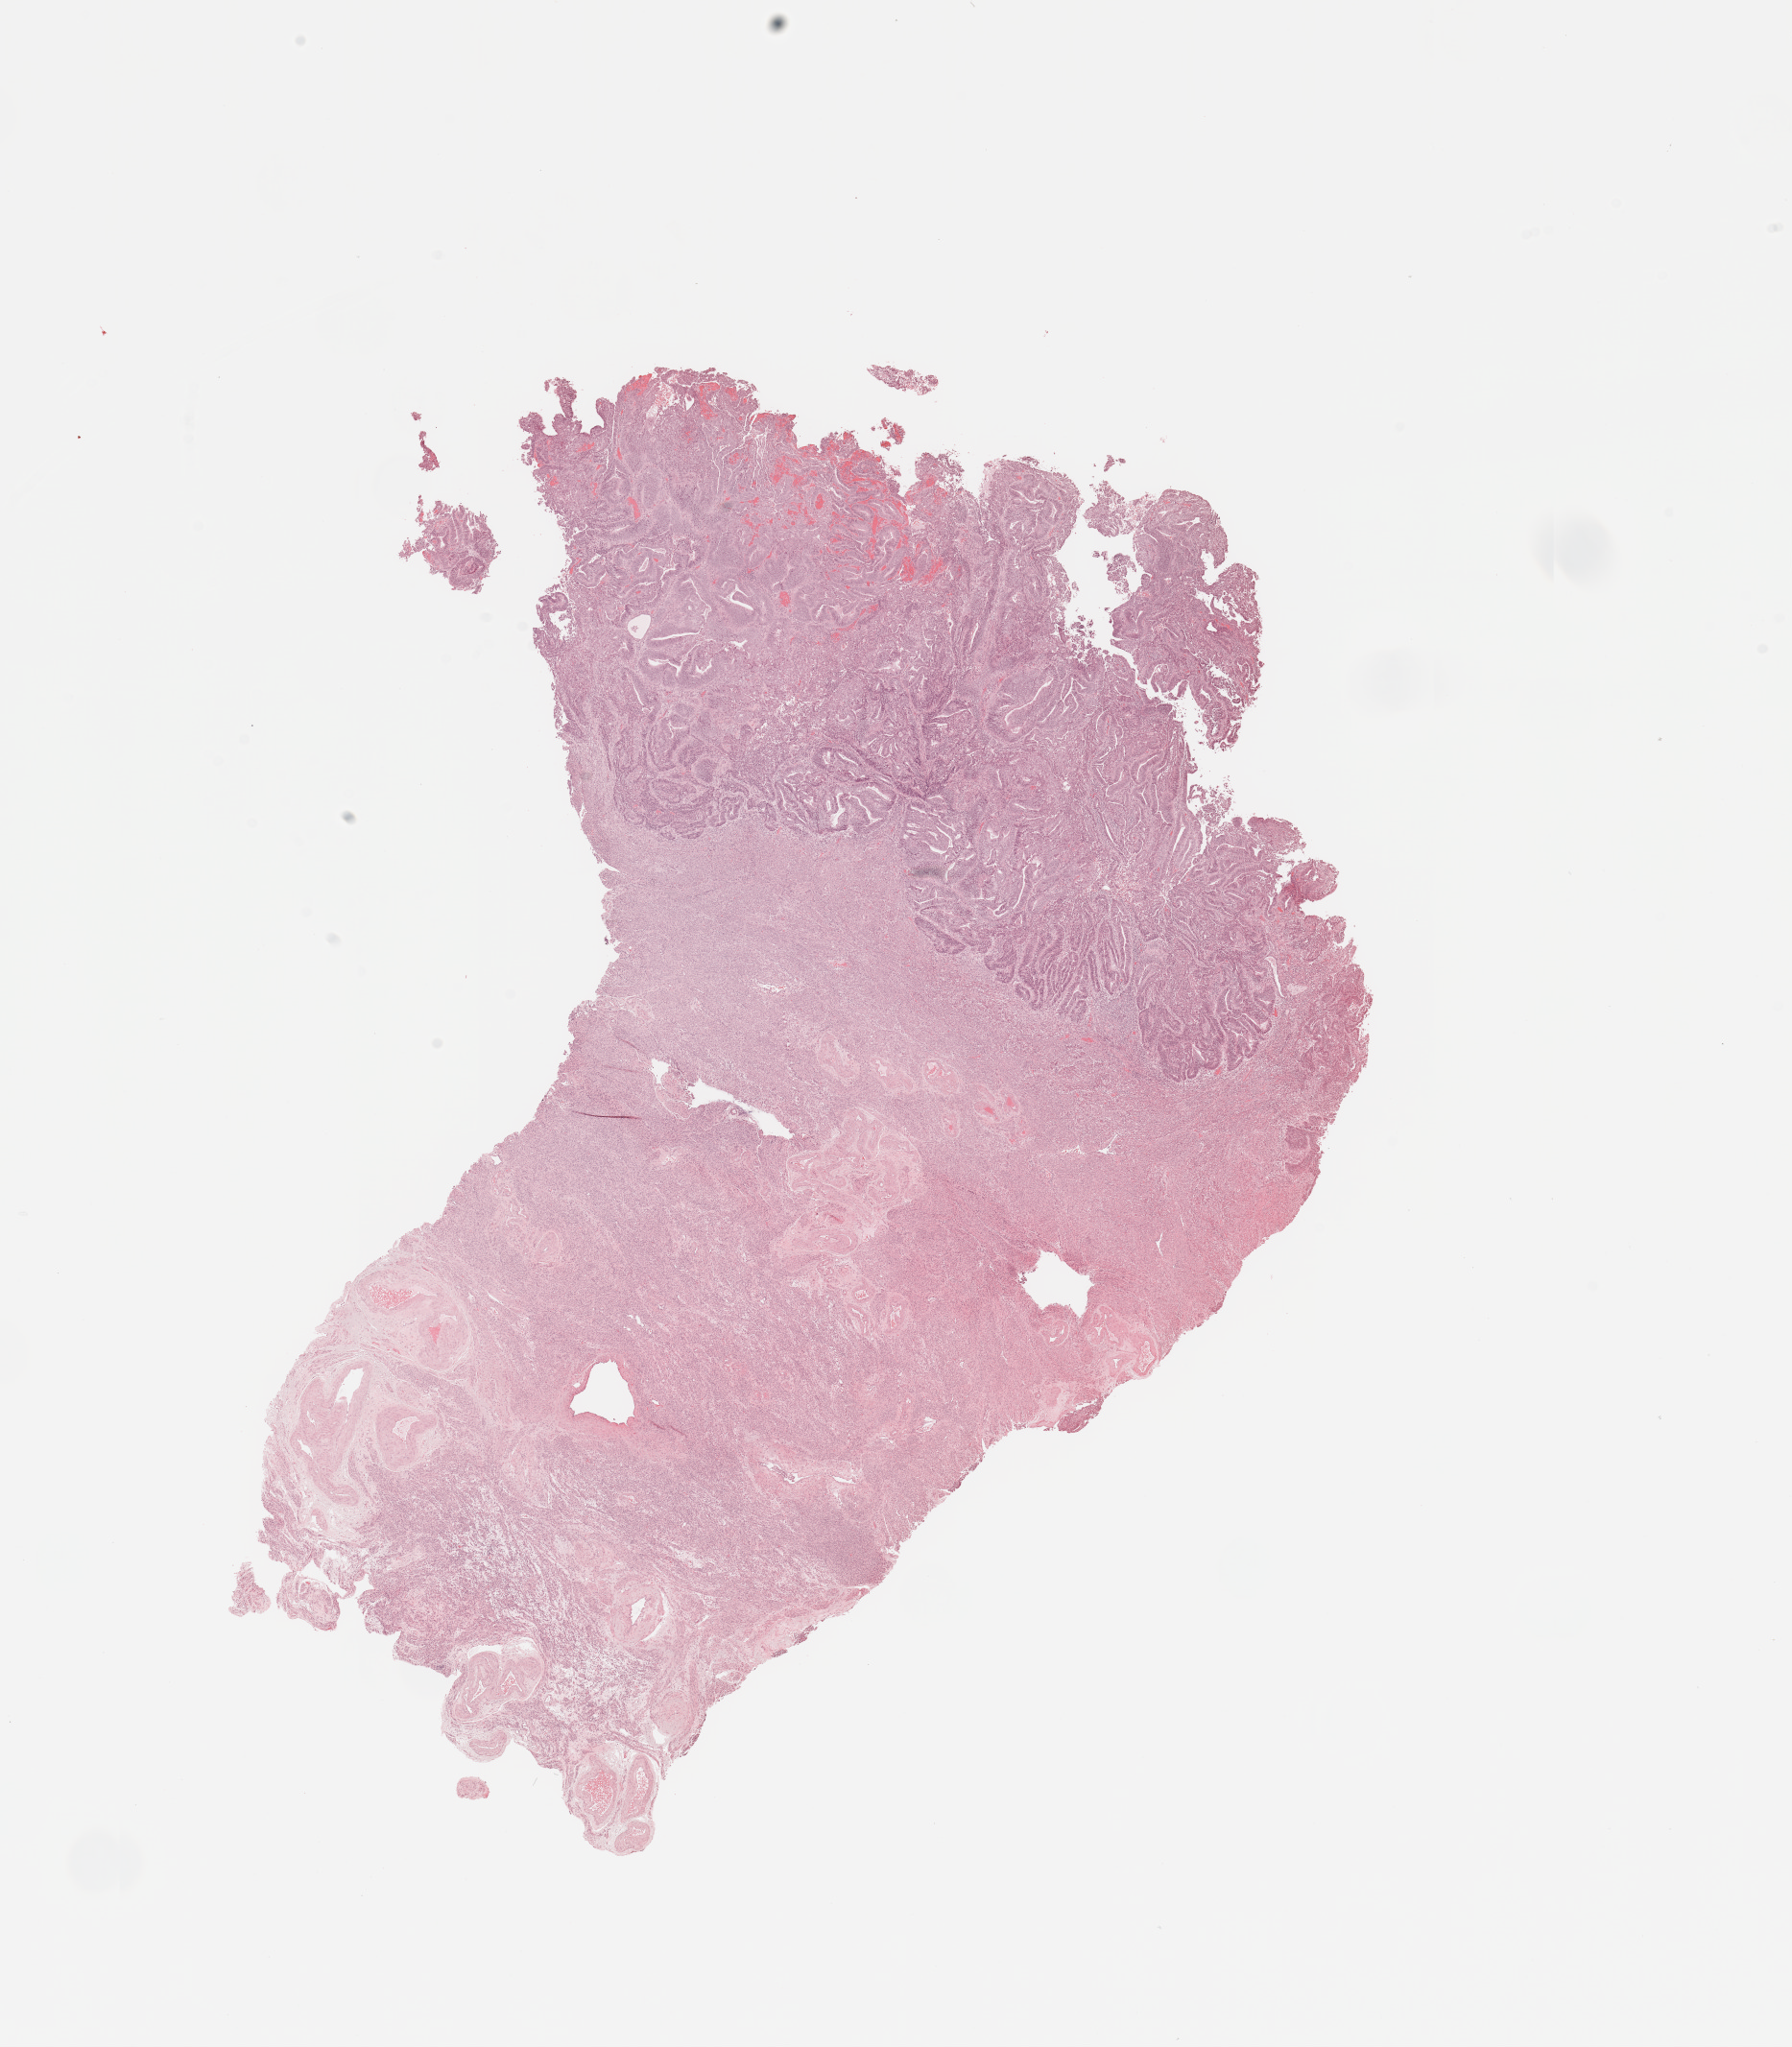
Whole-slide histology image, Hematoxylin and eosin (H&E) stained — a low-resolution overview of the entire scanned area, about 14.8 x 16.9 mm (from a 20x scan); tumour tissue sample, sampled site: uterus. Patient: female, age 86 years. Histologic grade: G2 (moderately differentiated). Pathologist review of this section (percent, as recorded): tumour nuclei 80%, necrosis 0%.
Primary tumour site (as recorded): posterior endometrium. Histologic diagnosis: Endometrioid adenocarcinoma, NOS. AJCC pathologic stage: III.